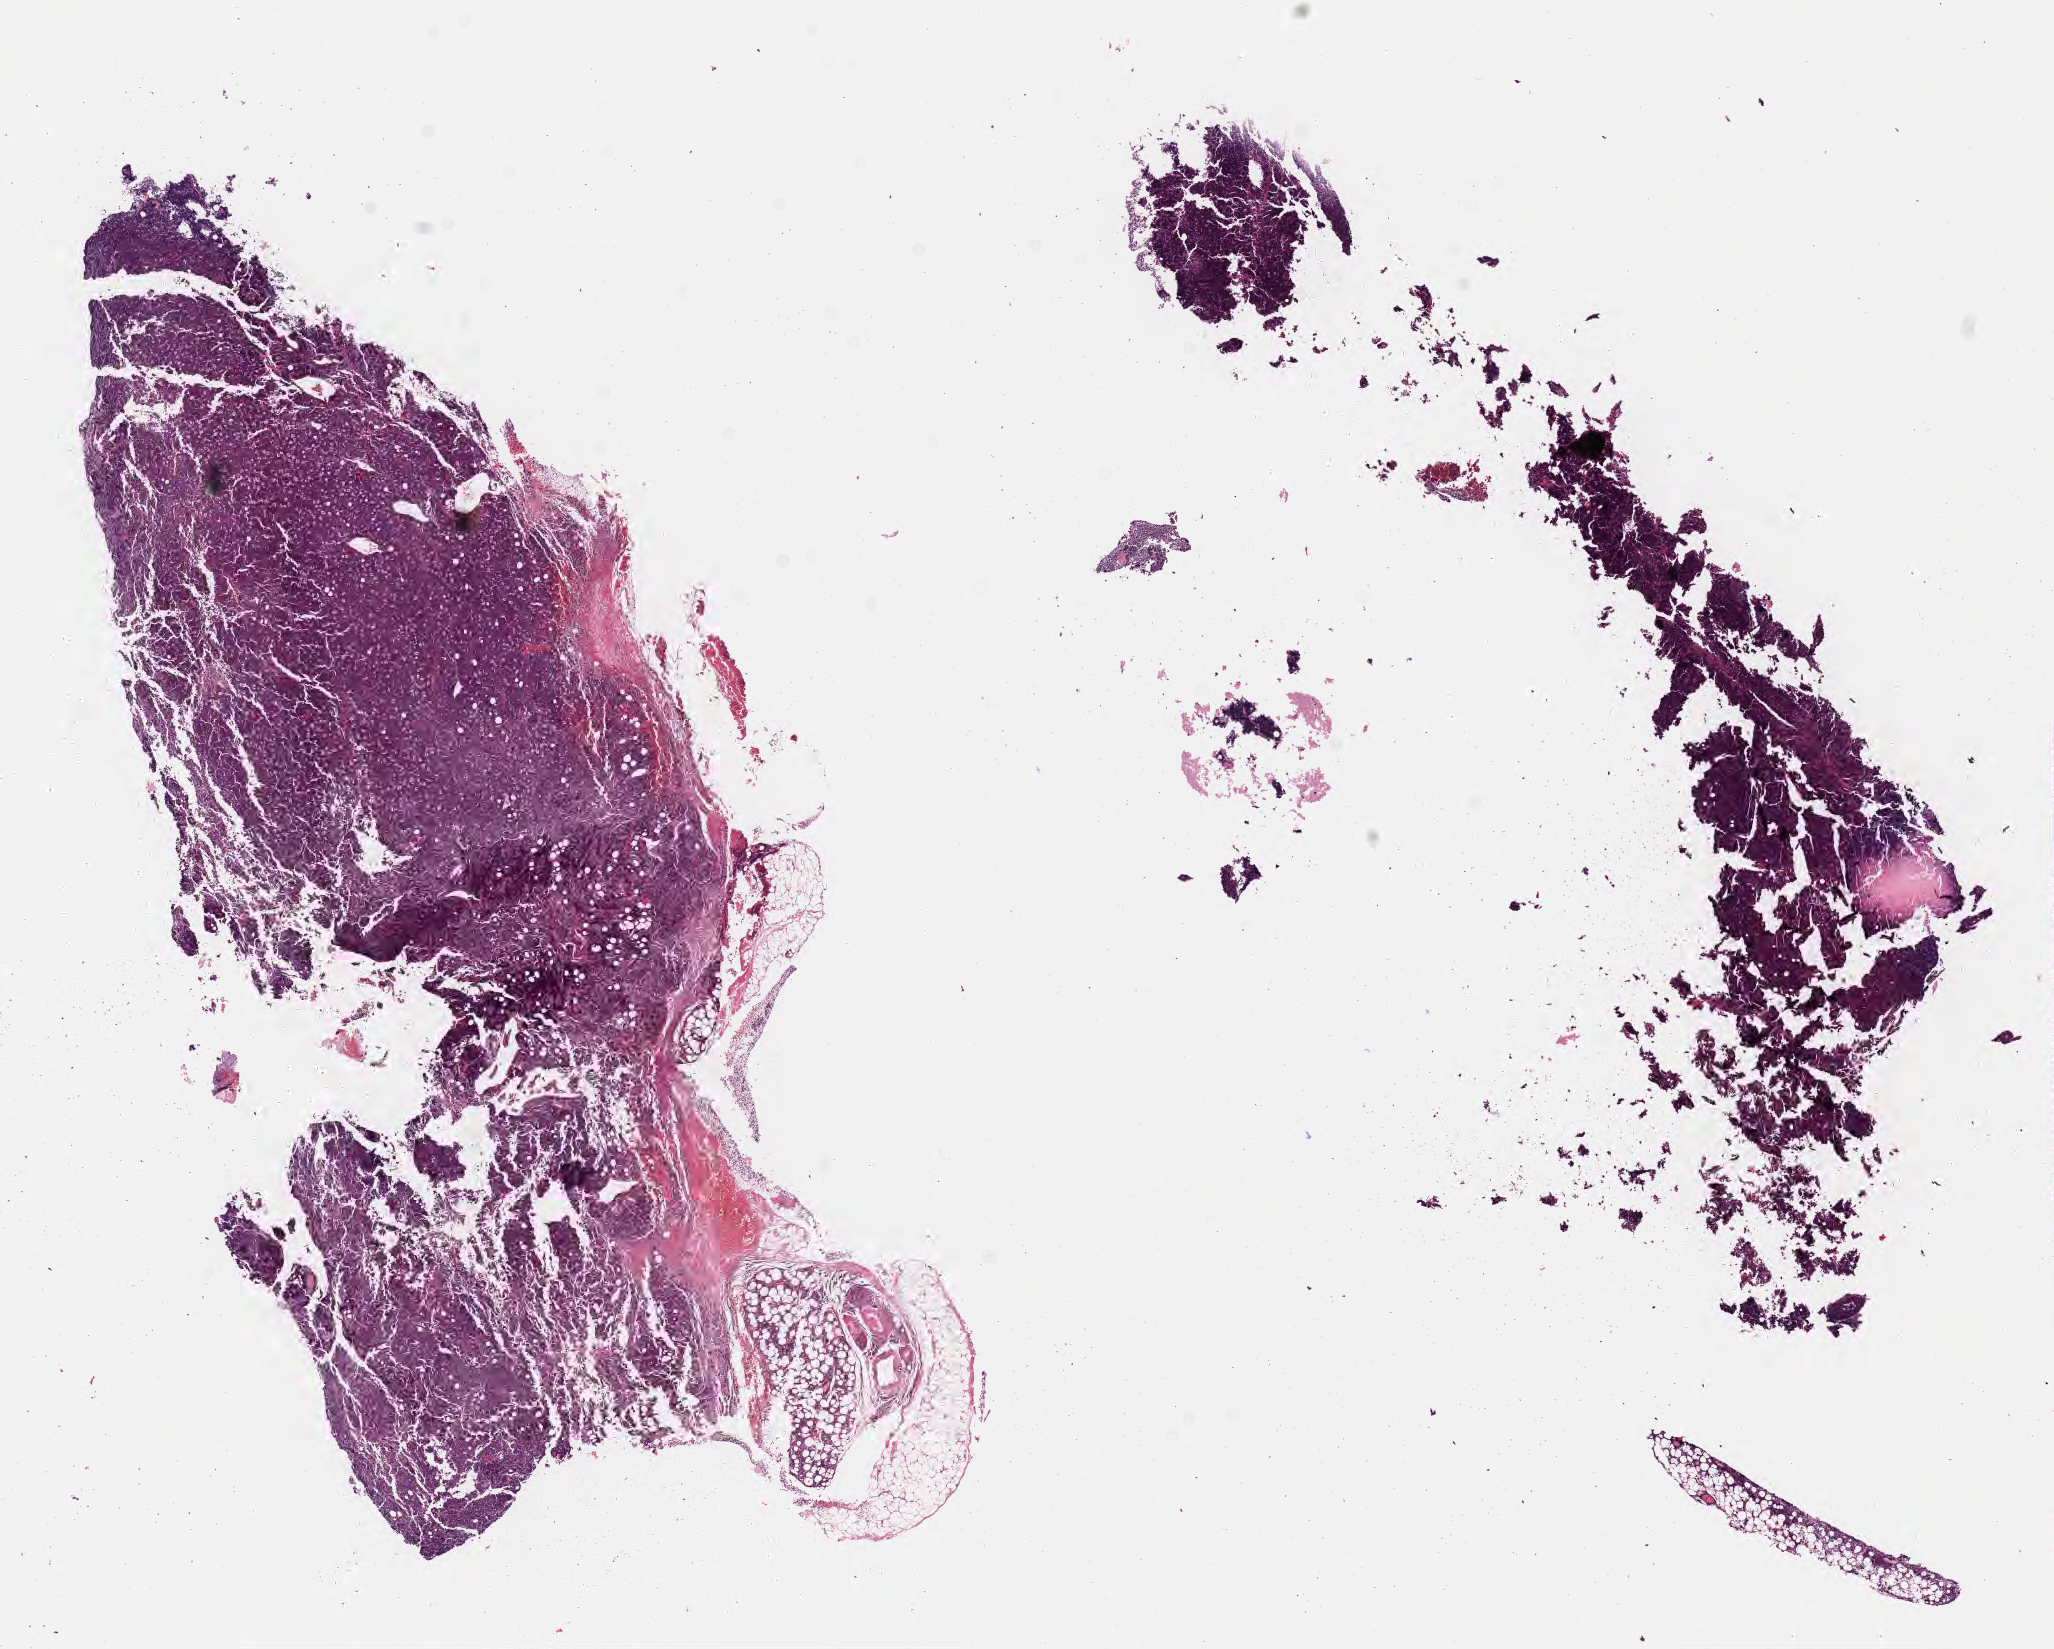
Hematoxylin and eosin (H&E) whole-slide image — low-resolution overview of the scanned area, about 16.6 x 13.3 mm, formalin-fixed paraffin-embedded section, specimen: primary tumor. Patient: female, 16 years old. Pathologist review of this section (percent, as recorded): tumor cells 90%, tumor nuclei 95%, stromal cells 10%, necrosis 0%, normal cells 0%. Infiltration values recorded for this section: lymphocyte infiltration 50%, monocyte infiltration 25%, neutrophil infiltration 0%.
Diagnosis: Burkitt lymphoma, NOS. Section: top of the tissue portion. Ann Arbor stage (patient): Stage IV.